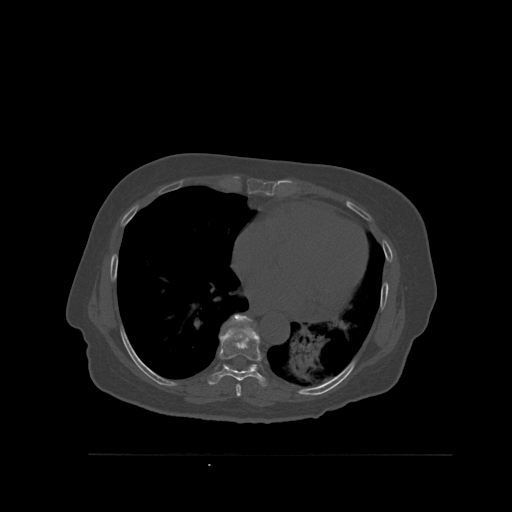
CT including the spine, one axial slice; slice 349 of 527 in the series (ordered by position); bone window (W 1800 / L 400 HU); 1.5 mm slice thickness; 512 × 512 image matrix, field of view 470 × 470 mm. Female patient, age 73 years. Case-level facts recorded for this patient, not image findings: primary cancer: breast; vertebrae with lytic lesions (as recorded): L2.
Structures marked on this image (semi-automatically segmented with operator editing):
- T7 vertebra: bounding box (x1, y1, x2, y2) in pixels: (236, 384, 241, 397)
- T8 vertebra: (208, 328, 267, 387)
- T9 vertebra: (224, 314, 258, 368)